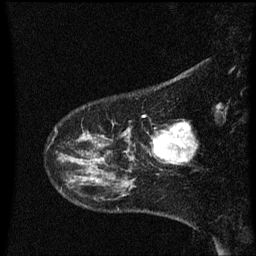
Breast MRI (dynamic contrast-enhanced), one sagittal slice. Slice 10 of 60 in the series (ordered by position). Dynamic contrast-enhanced series, image 2 of 3 at this slice position (ordered by acquisition). 1.5 T. TE 4.2 ms, TR 8.4 ms. 2 mm slice thickness. 256 × 256 image matrix. Female patient, age 41 years. From the clinical record (not read from this slice): setting: breast cancer imaged before/during neoadjuvant chemotherapy; receptor status: triple-negative.
Outlined on this slice (semi-automatic segmentation, software-assisted and operator-edited):
- analysis volume of interest (the breast-tissue region the enhancement analysis was run in; not a lesion): bounding box [x1, y1, x2, y2] px = [141, 116, 193, 175]
- tumour enhancement mask (voxels above the 70 % enhancement threshold inside the analysis volume of interest): [153, 124, 190, 163]